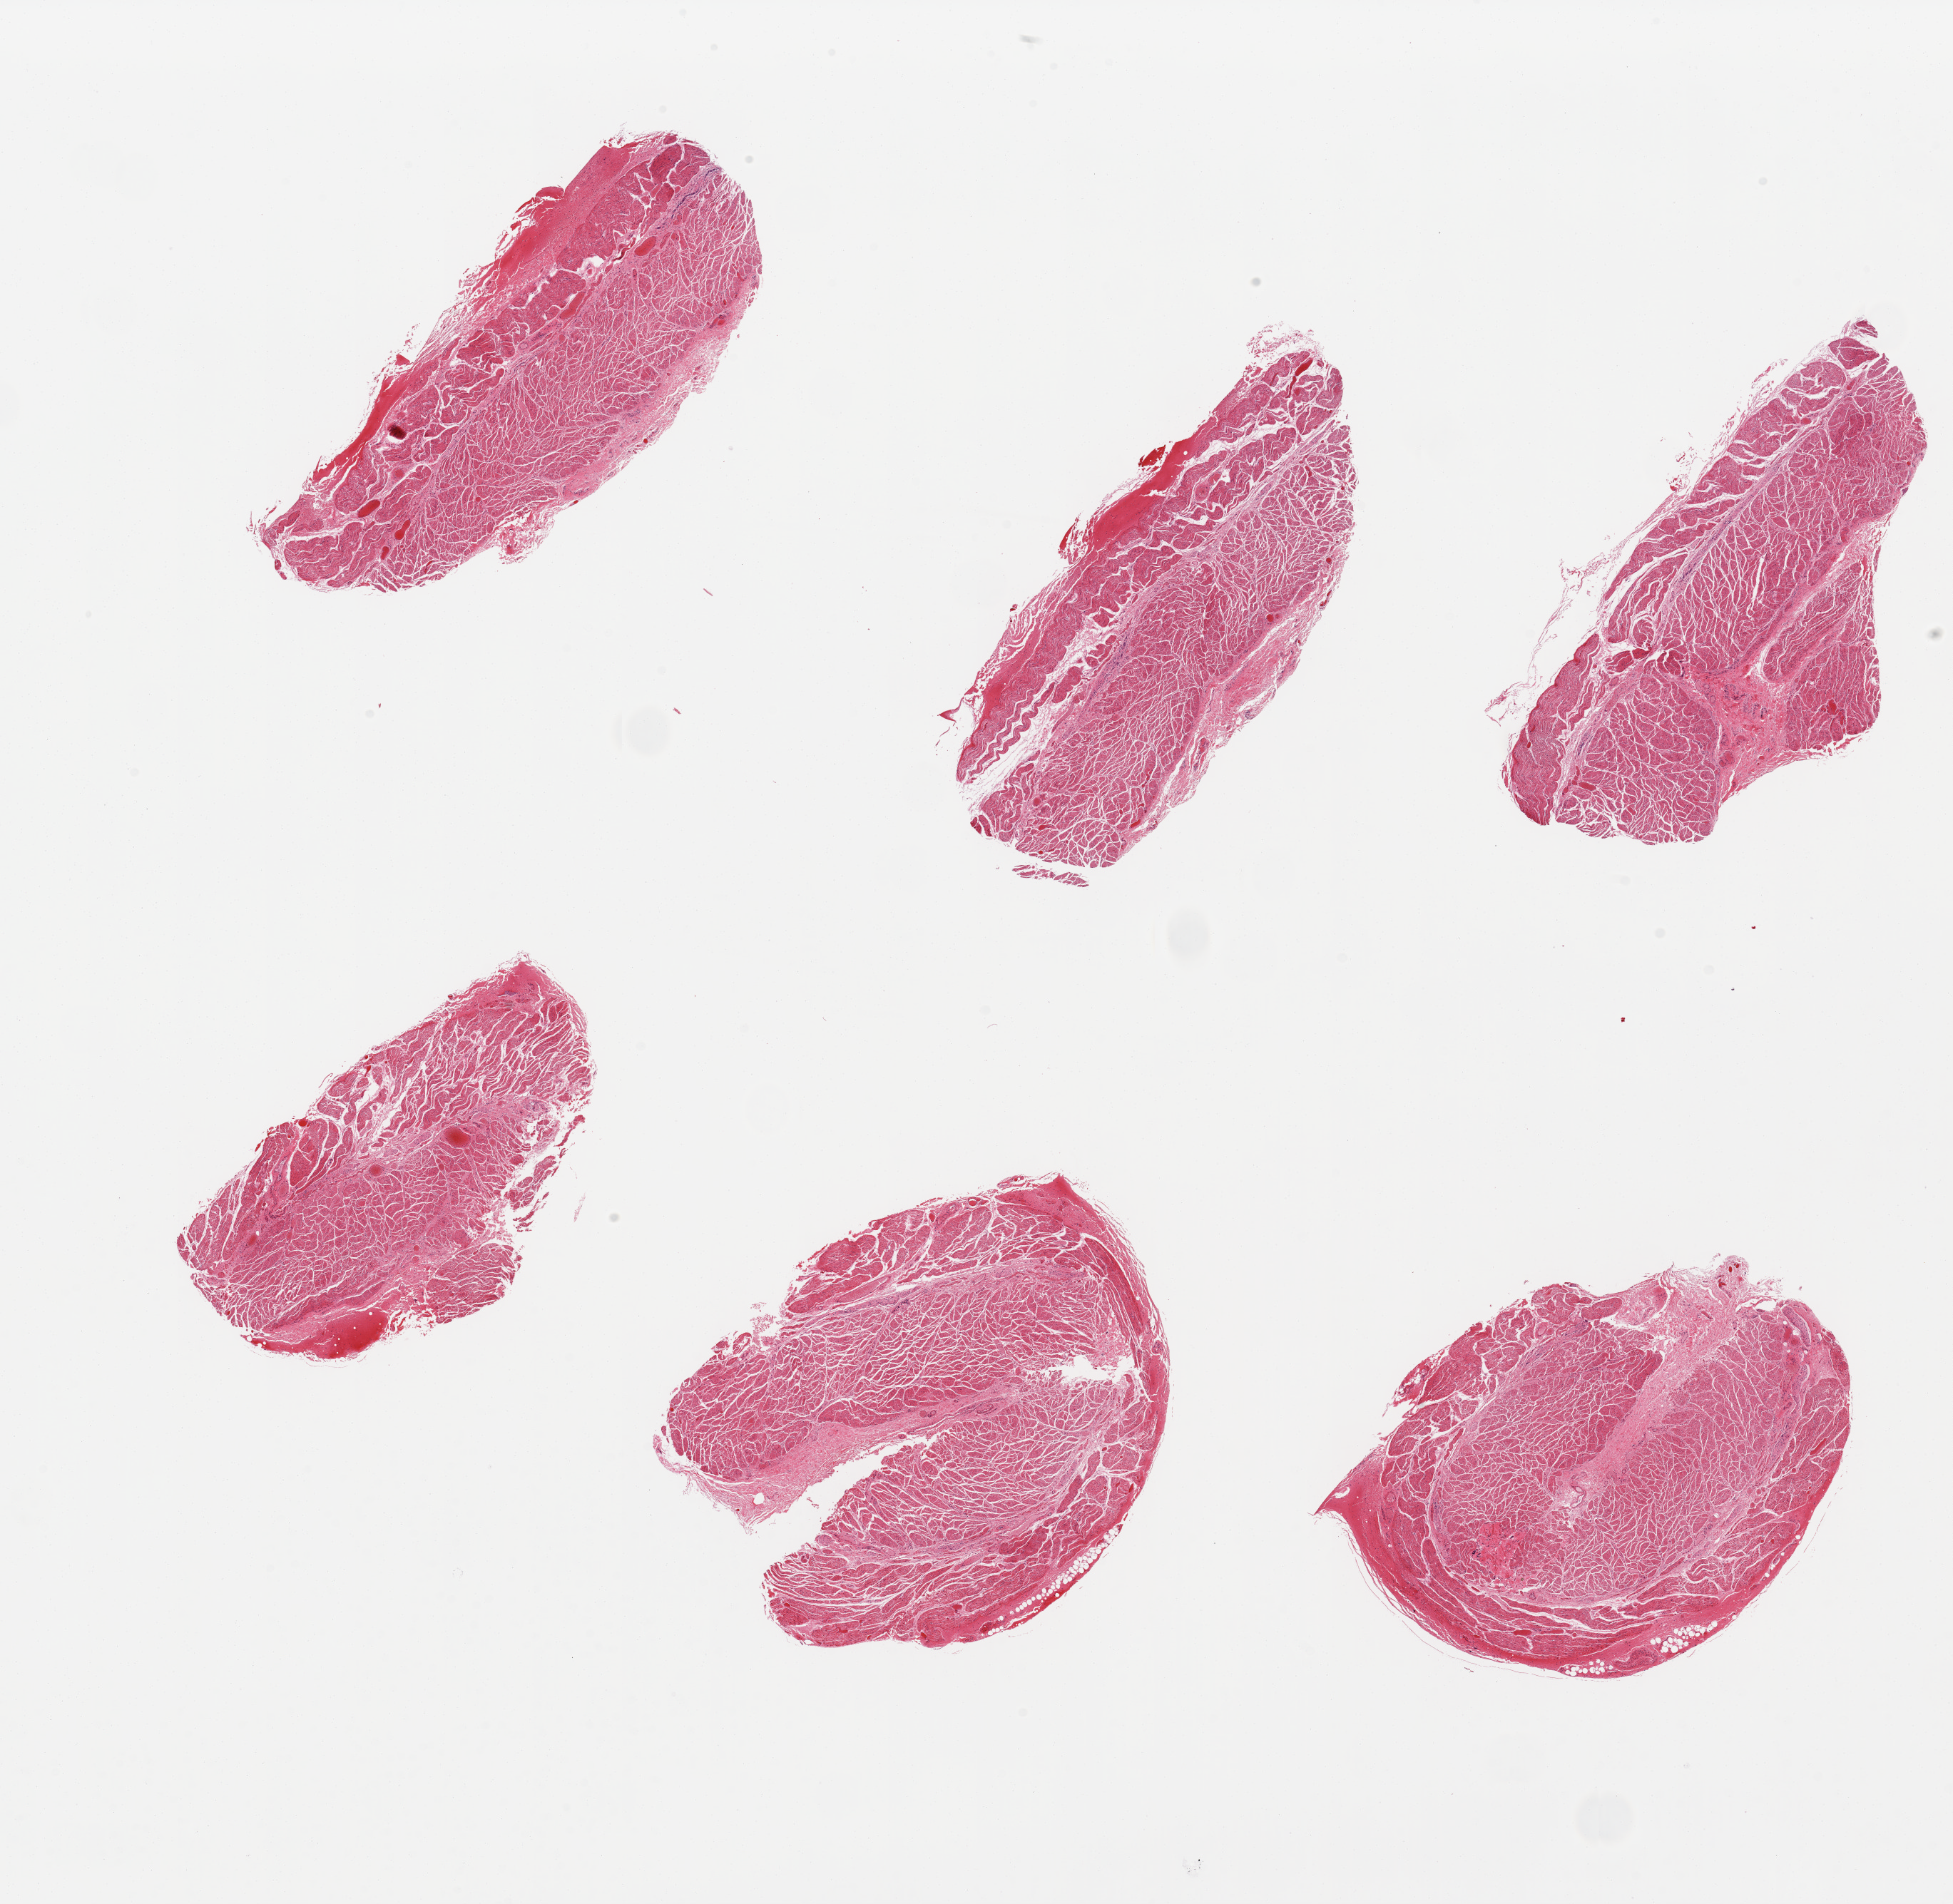
Whole-slide image, haematoxylin and eosin stain — shown as a low-resolution overview of the whole scanned area (about 21.7 x 21.1 mm, from a 20x scan). PAXgene-fixed paraffin-embedded (PFPE) section. Sampled site (target tissue): gastroesophageal junction. Donor tissue sample. Donor sex: male.
* pathologist's review note for this sample: 6 pieces; well trimmed